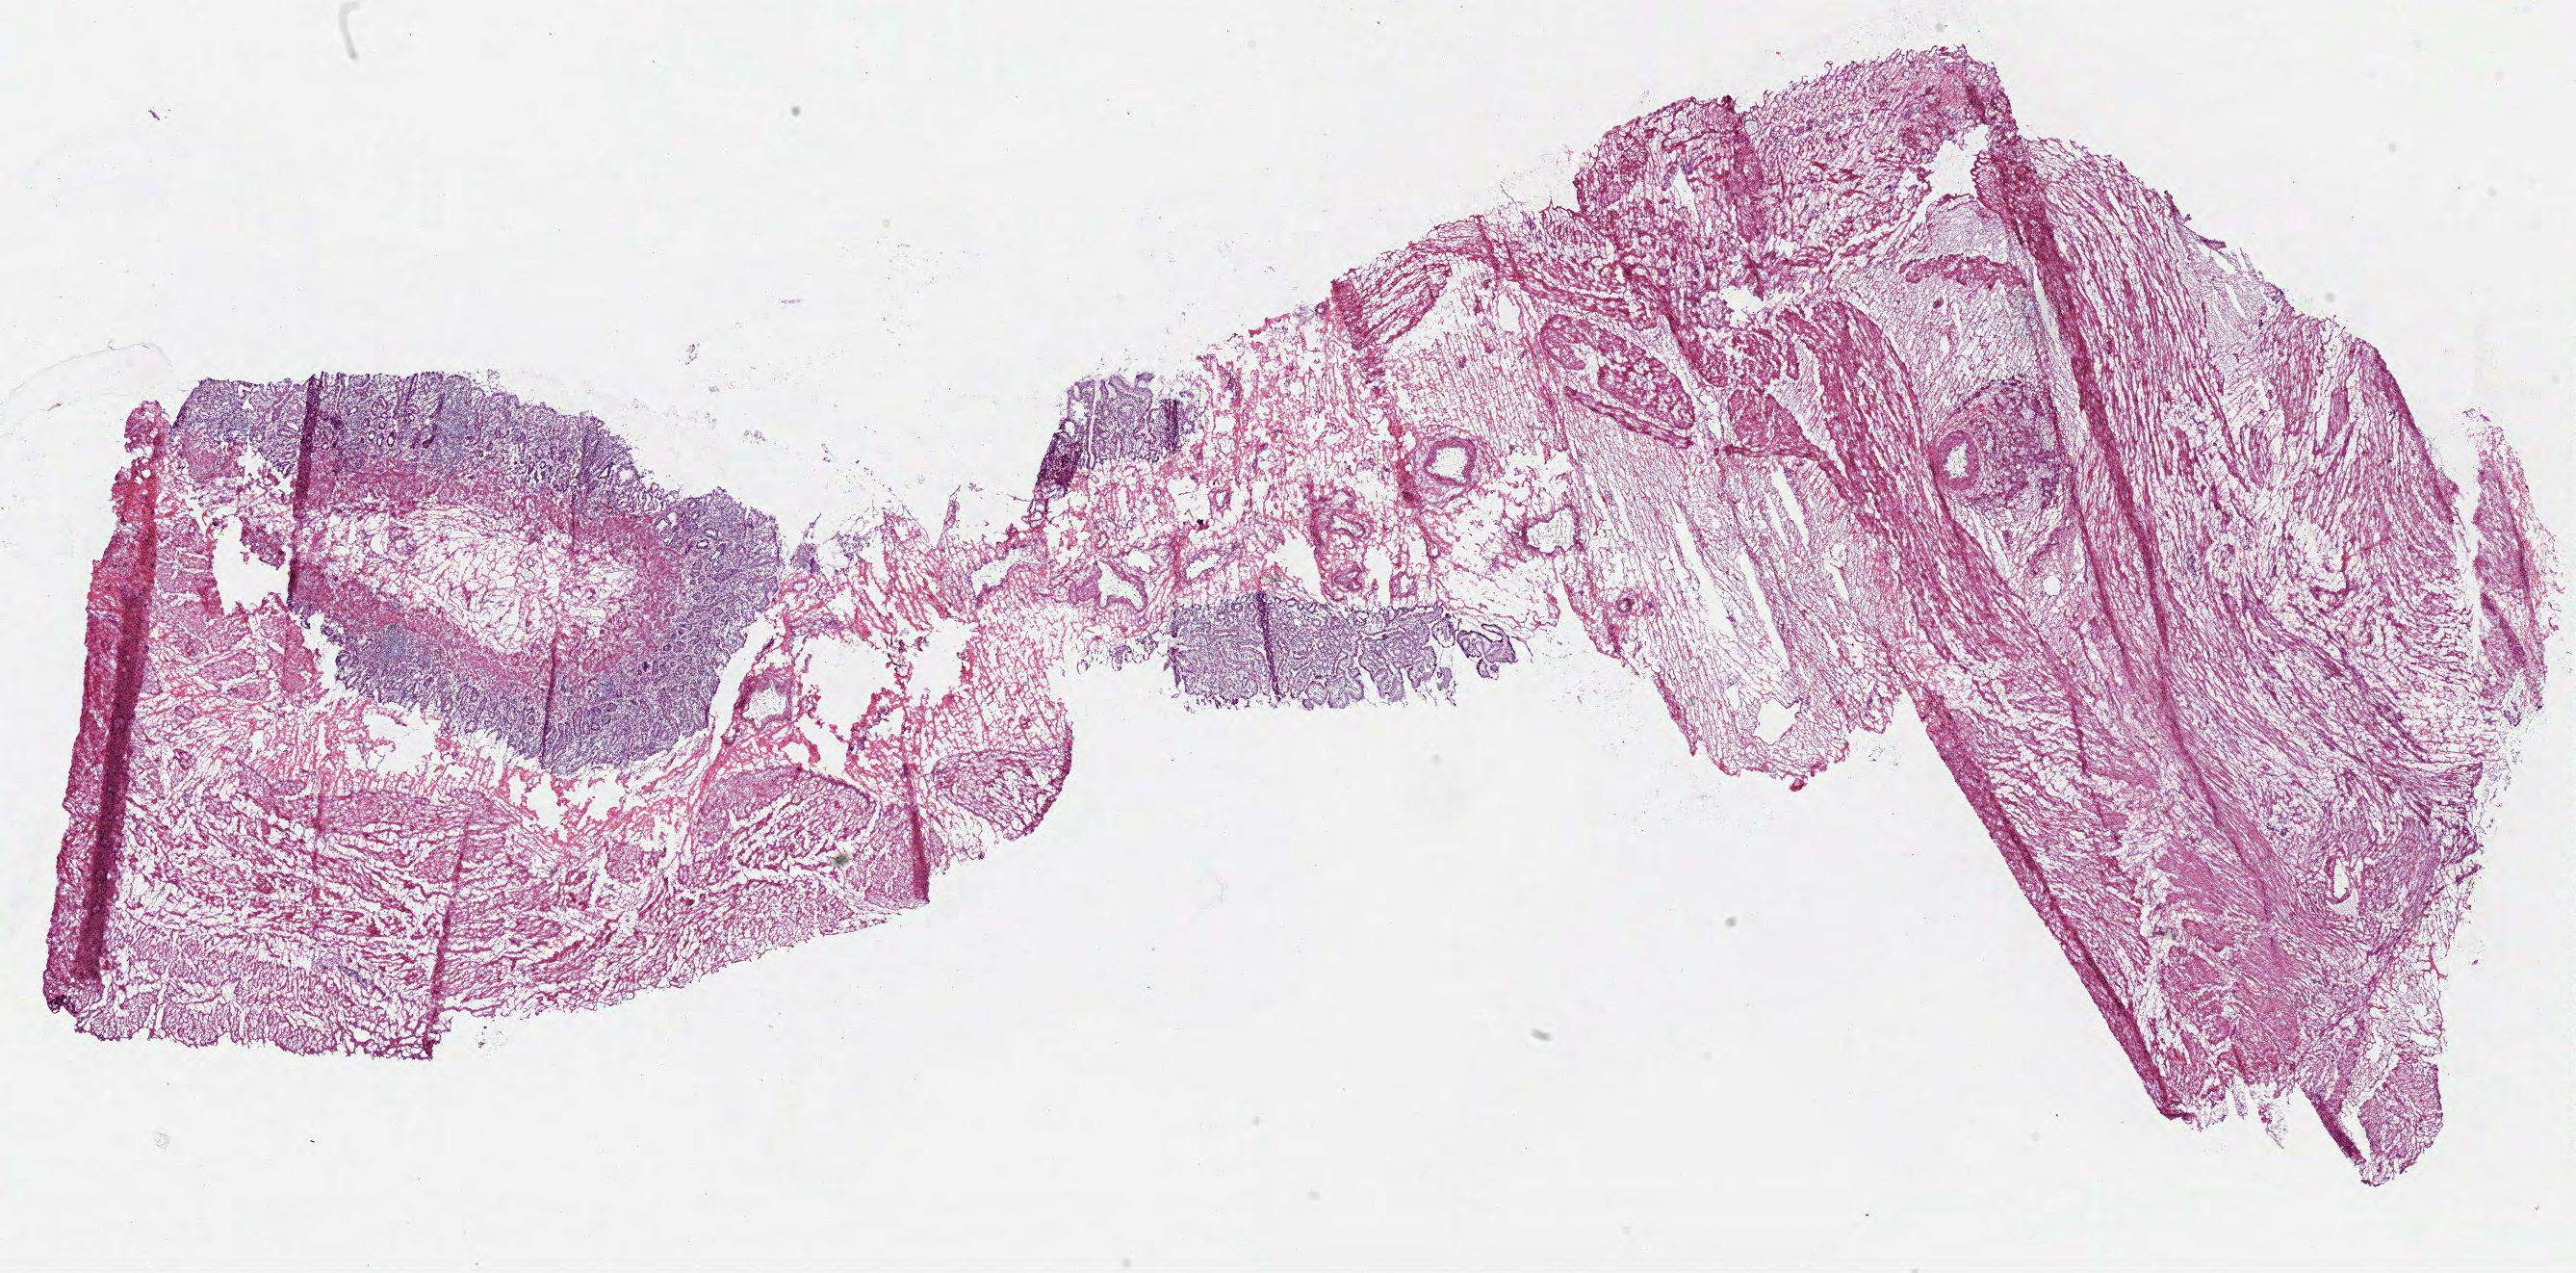
Digitized Hematoxylin and eosin (H&E) stained tissue section (whole slide) — a low-resolution overview of the entire scanned area, about 21.0 x 10.4 mm; frozen section from the top of the tissue portion; stomach, solid tissue normal (non-tumour tissue) sample. Female, age 46 years at initial diagnosis.
This section: solid tissue normal (non-tumour) sample from the same patient. Patient diagnosis: Adenocarcinoma, NOS (body of stomach).